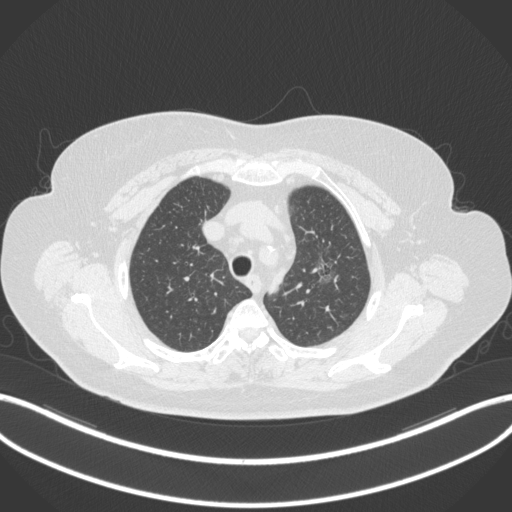
Chest CT, one axial slice. Slice 268 of 310 in the series (ordered by position). Reconstruction kernel B31f. 120 kVp. Lung window (W 1500 / L -600 HU). 1 mm slice thickness. 512 × 512 image matrix, field of view 400 × 400 mm. Patient: female, 70 years. Case-level facts recorded for this patient, not image findings: clinical TNM (as recorded): T1c N0 M0.
Structures marked on this image (bounding box drawn by a radiologist):
- lung tumour (recorded histology: adenocarcinoma): box from (x=308, y=256) to (x=341, y=292) px